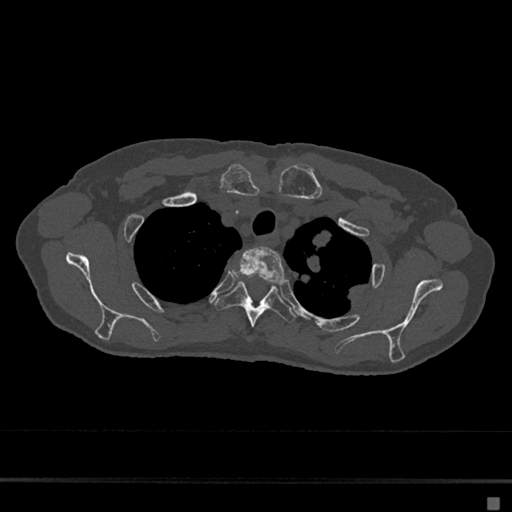
CT including the spine, one axial slice; slice 553 of 797 in the series (ordered by position); reconstruction kernel Br40s/3; 120 kVp; bone window (W 1800 / L 400 HU); 512 × 512 image matrix, field of view 360 × 360 mm. Female patient, age 68 years. From the clinical record (not read from this slice): primary cancer: renal.
Annotated regions visible in this slice (semi-automatically segmented with operator editing):
- T2 vertebra: bounding box <232,247,286,283> (left, top, right, bottom; pixels)
- T3 vertebra: <215,281,296,327>